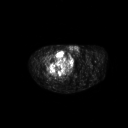
FDG PET of an extremity soft-tissue mass (from a PET/CT study), one axial slice. Slice 276 of 311 in the series (ordered by position). 3.27 mm slice thickness. 128 × 128 image matrix. Patient: male, 50 years. Case-level facts recorded for this patient, not image findings: histological type: undifferentiated - pleiomorphic; grade: high; site of the primary tumour: right thigh.
Structures marked on this image (expert contour drawn on MRI and transferred to this co-registered scan by the dataset authors):
- gross tumour volume including surrounding oedema: bounding box (x1, y1, x2, y2) in pixels: (47, 50, 66, 68)
- gross tumour volume (mass): (47, 50, 66, 69)